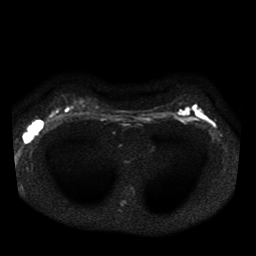
Breast MRI, one axial slice. Position 28 of 41 along the scan axis. Diffusion-weighted series; image 2 of 4 stored at this slice position (different b-values; order by instance number). 1.5 T. 256 × 256 image matrix, field of view 330 × 330 mm. Female patient.
Structures marked on this image (expert manual segmentation):
- tumour on diffusion-weighted imaging: box from (x=26, y=122) to (x=39, y=141) px